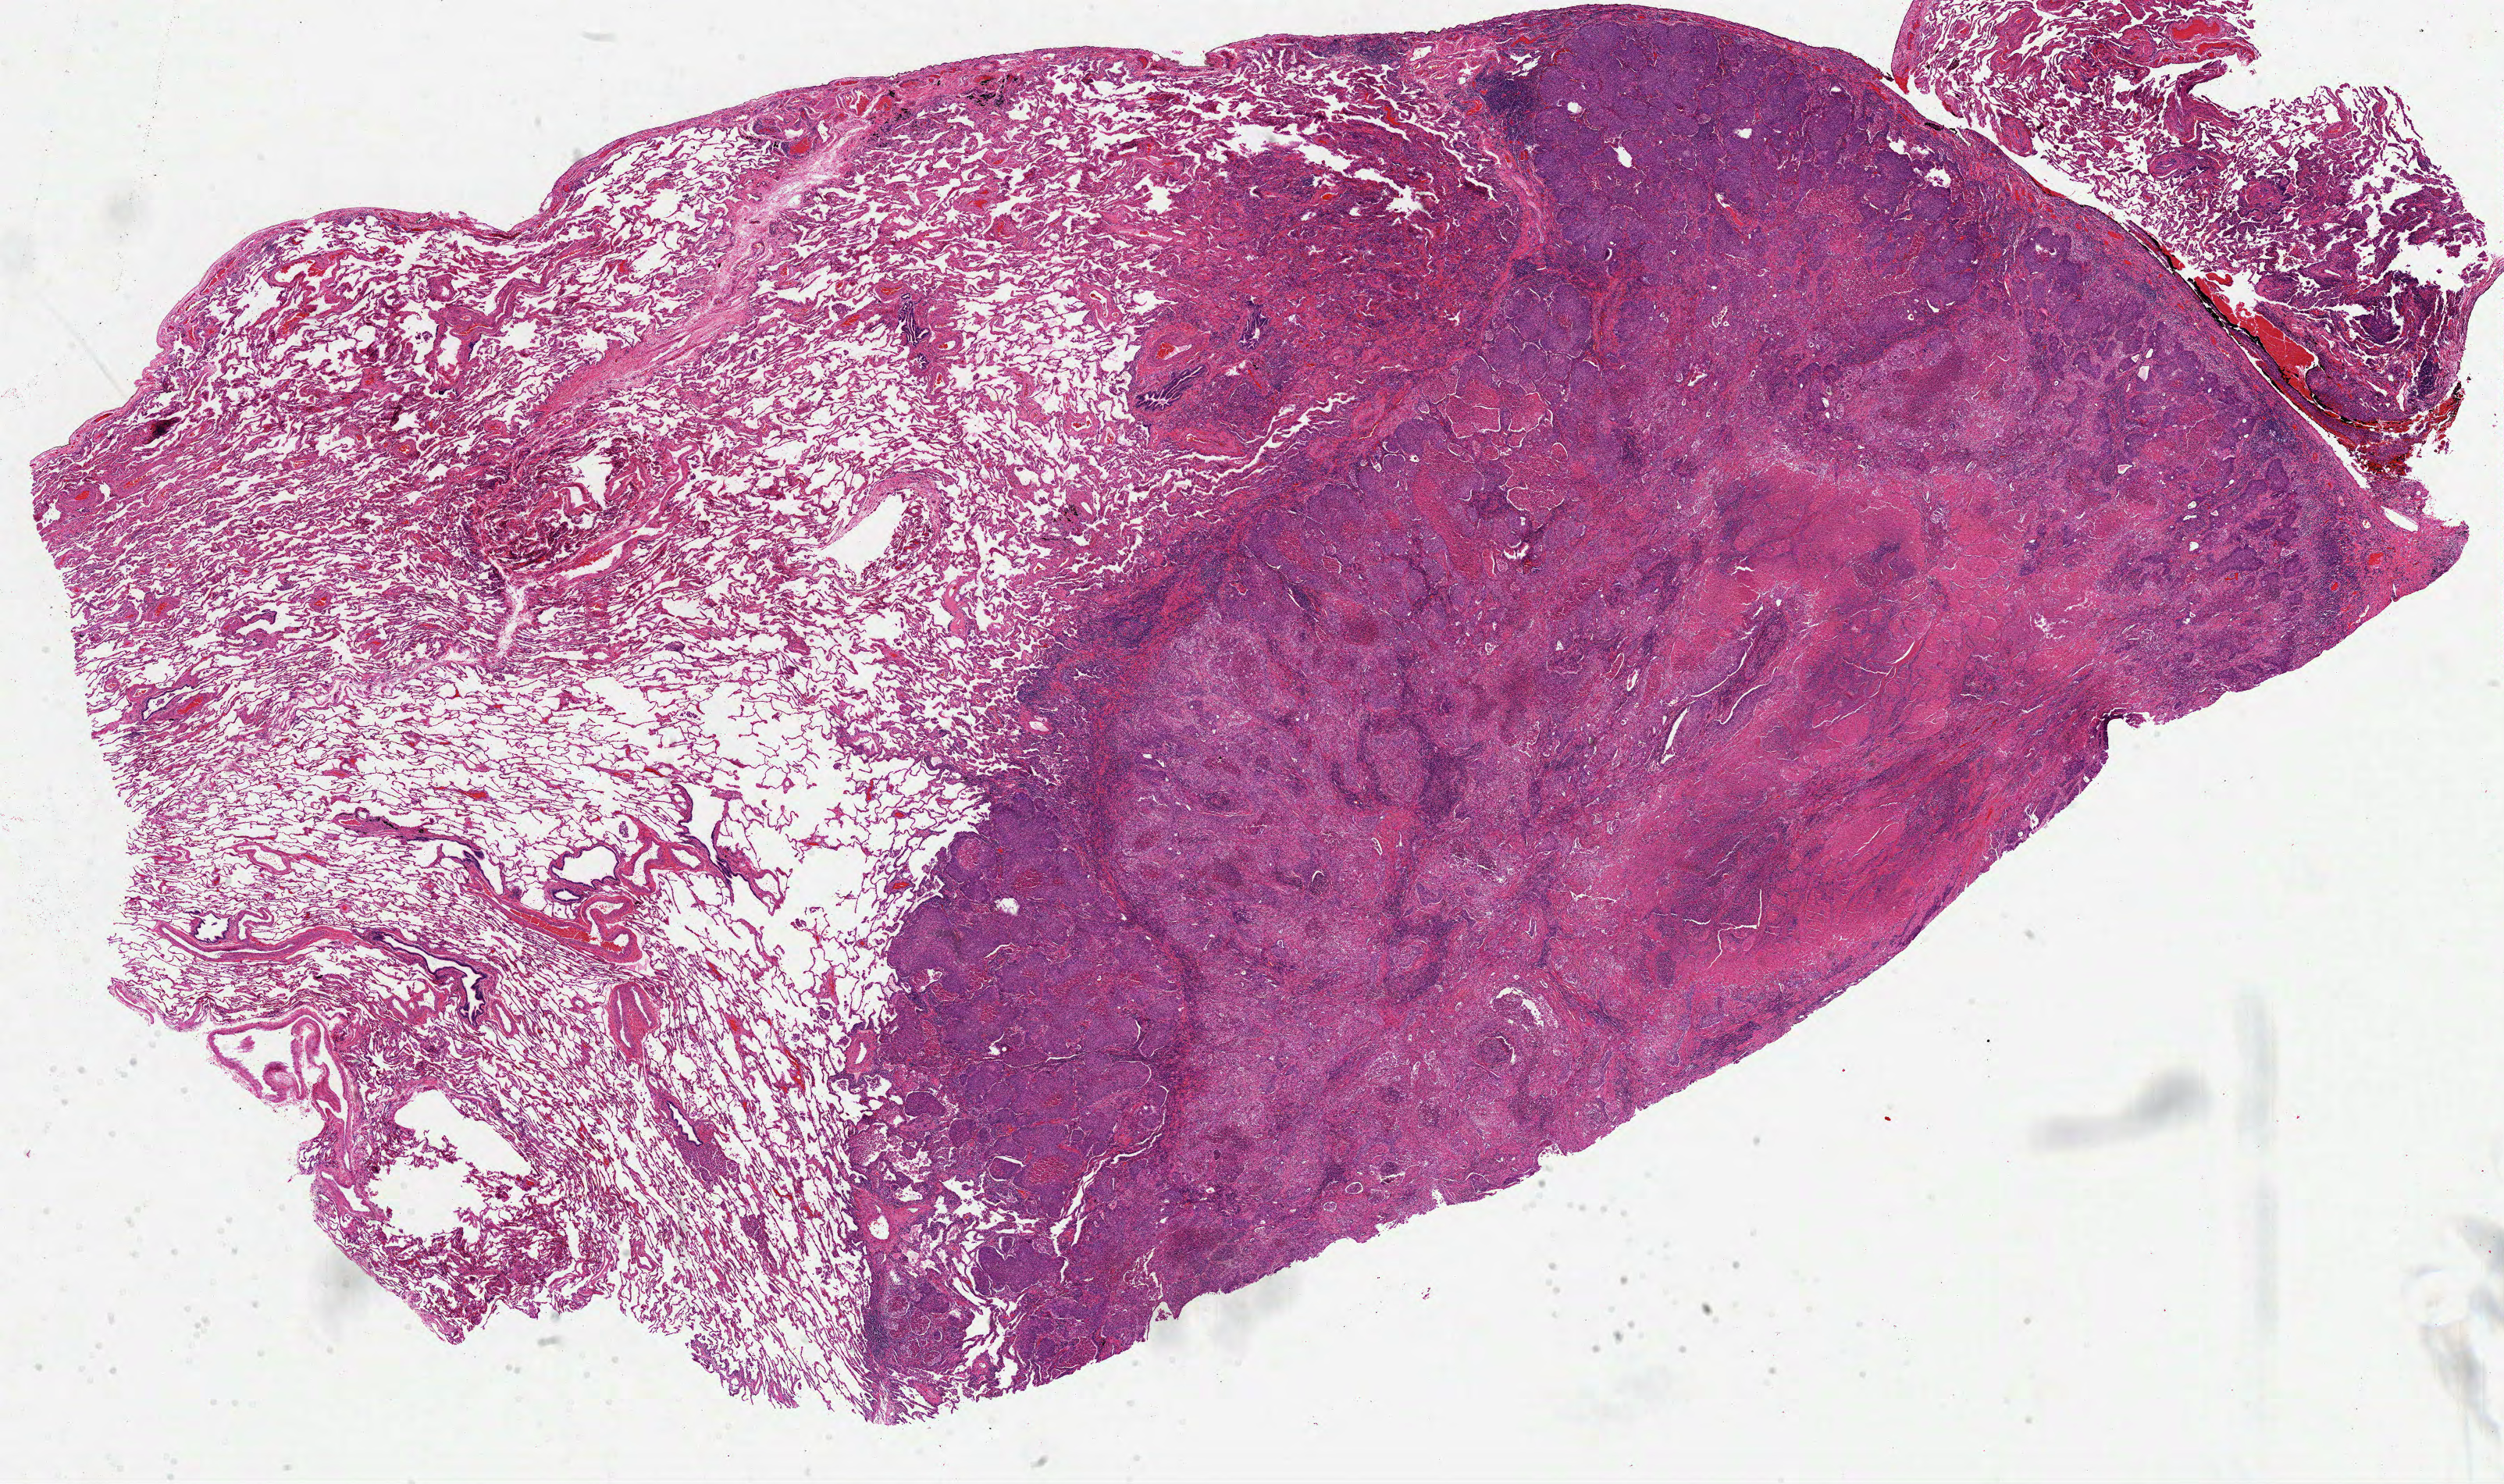
Whole-slide histology image, H&E-stained, shown as a low-resolution overview of the whole scanned area (about 25.9 x 15.3 mm, from a 40x scan); formalin-fixed paraffin-embedded (FFPE) diagnostic section; primary tumour sample from the lung. Patient: male, age at initial diagnosis 68 years.
Pathologic diagnosis: Squamous cell carcinoma, NOS (upper lobe, lung).